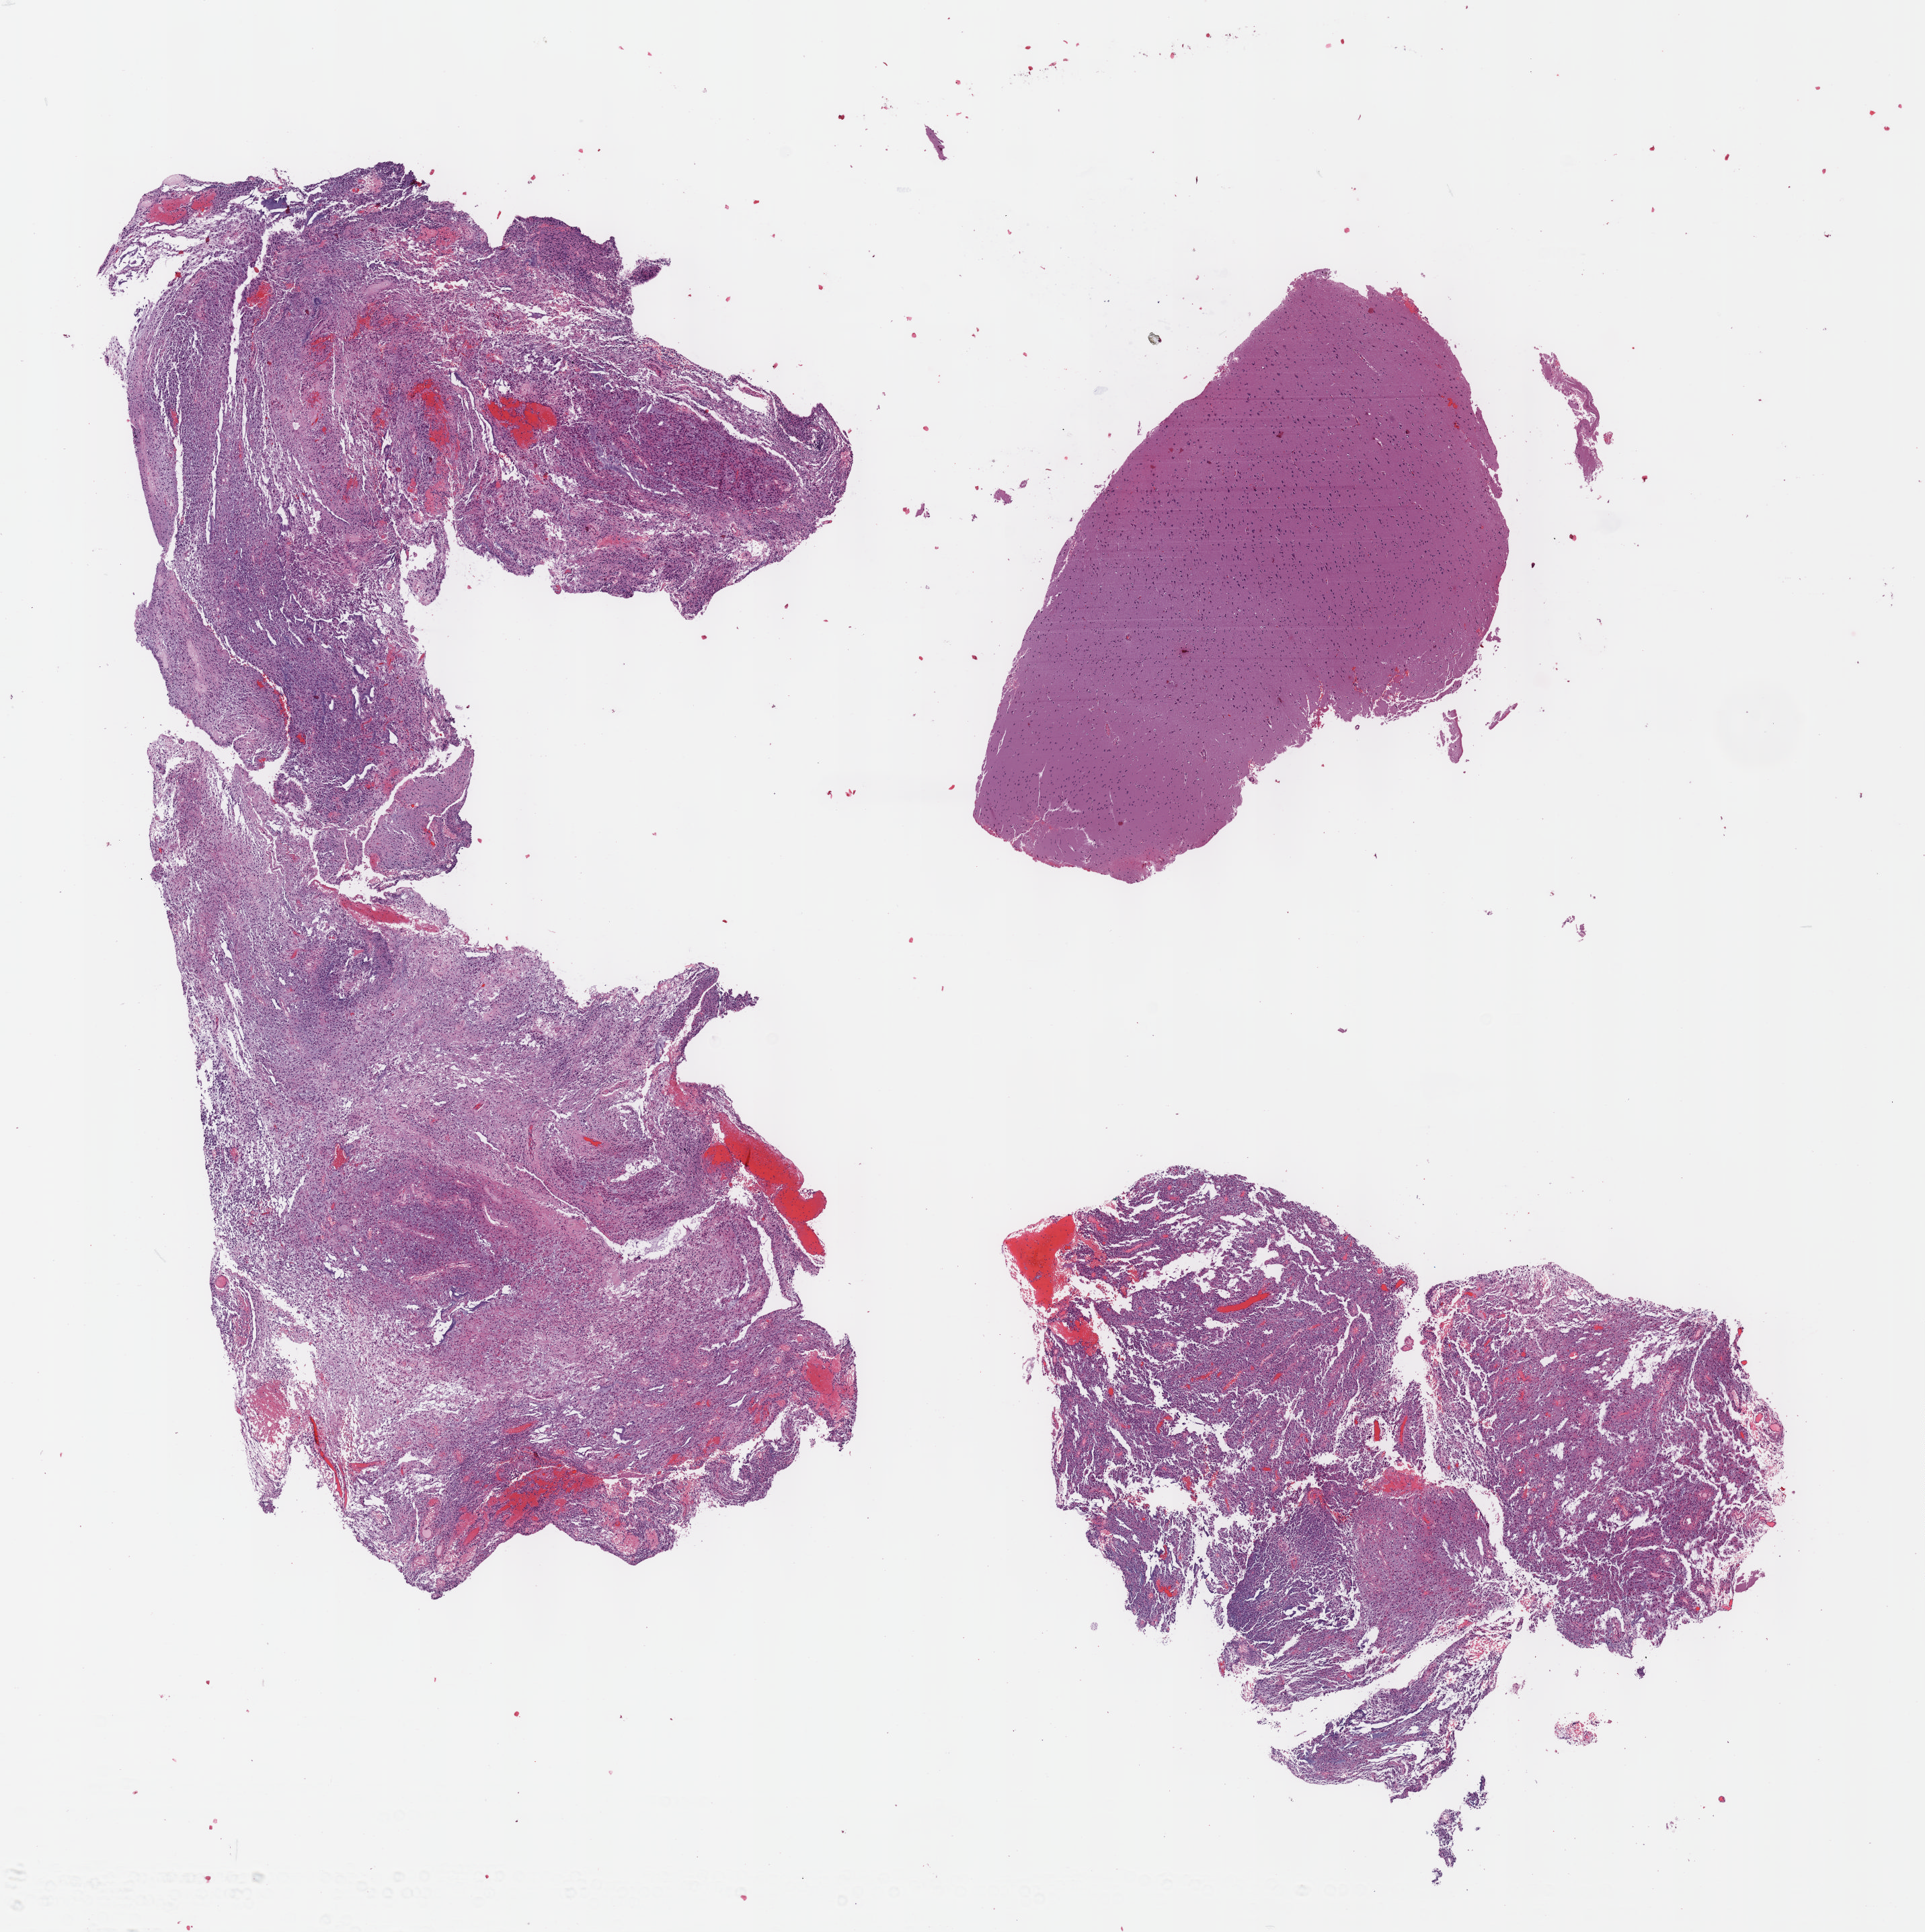
H&E whole-slide image, a low-resolution overview of the entire scanned area, about 11.6 x 11.6 mm (acquisition: 40x scan), formalin-fixed paraffin-embedded (FFPE) diagnostic section, sample: primary tumour, brain. Male, age 33 years at initial diagnosis. Histologic grade: G2 (moderately differentiated).
Pathologic diagnosis: Mixed glioma (cerebrum).